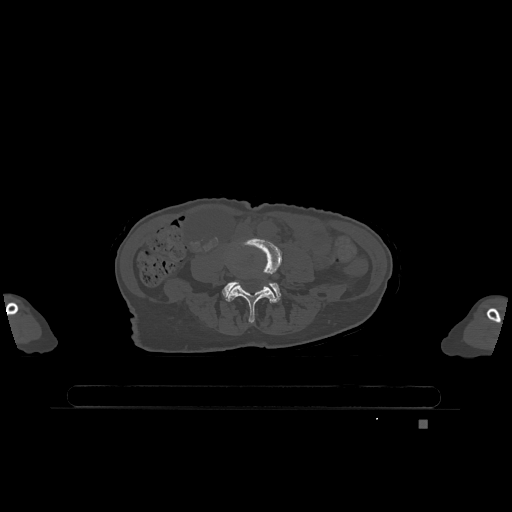
CT including the spine, one axial slice; slice 281 of 1317 in the series (ordered by position); bone window (W 1800 / L 400 HU); 0.5 mm slice thickness; 512 × 512 image matrix, field of view 500 × 500 mm. Patient: female, 74 years. From the clinical record (not read from this slice): primary cancer: lung; vertebrae with lytic lesions (as recorded): T1, T4, T5, T6, L4, L5.
Structures marked on this image (semi-automatically segmented with operator editing):
- L4 vertebra: box from (x=226, y=238) to (x=282, y=323) px
- L5 vertebra: (x=222, y=281)–(x=281, y=302)